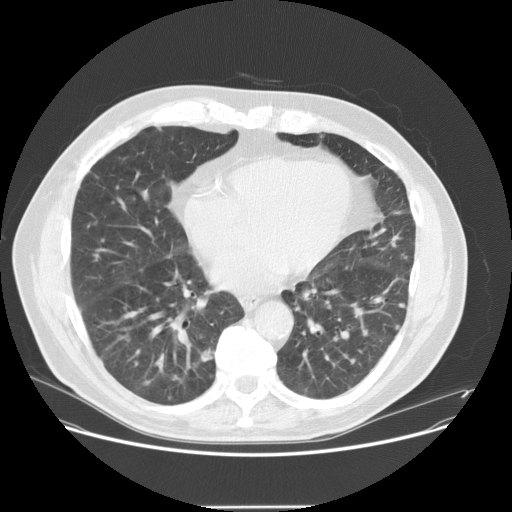
Low-dose screening chest CT, one axial slice; position 60 of 143 along the scan axis; reconstruction kernel STANDARD; lung window (W 1500 / L -600 HU); 512 × 512 image matrix, field of view 400 × 400 mm.
Annotated regions visible in this slice (outlined manually by an expert reader):
- lesion 1 (tumor, lower lobe of right lung): box from (x=200, y=349) to (x=214, y=362) px